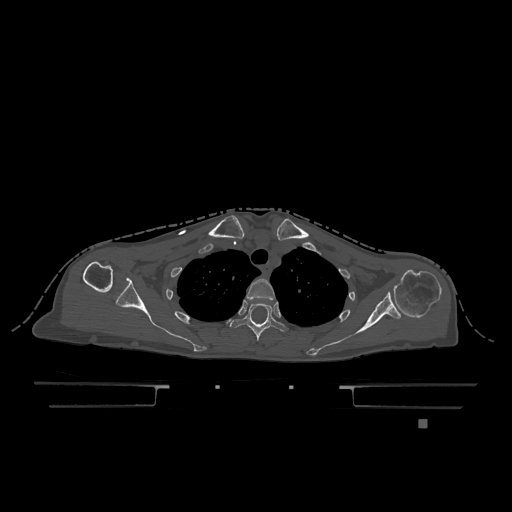
CT including the spine, one axial slice; position 934 of 1317 along the scan axis; bone window (W 1800 / L 400 HU); 0.5 mm slice thickness; 512 × 512 image matrix. Patient: female, 74 years. Case-level facts recorded for this patient, not image findings: primary cancer: lung; vertebrae with lytic lesions (as recorded): T1, T4, T5, T6, L4, L5.
Annotated regions visible in this slice (semi-automatically segmented with operator editing):
- T2 vertebra: bounding box [x1, y1, x2, y2] px = [246, 279, 275, 301]
- T3 vertebra: [230, 303, 288, 341]